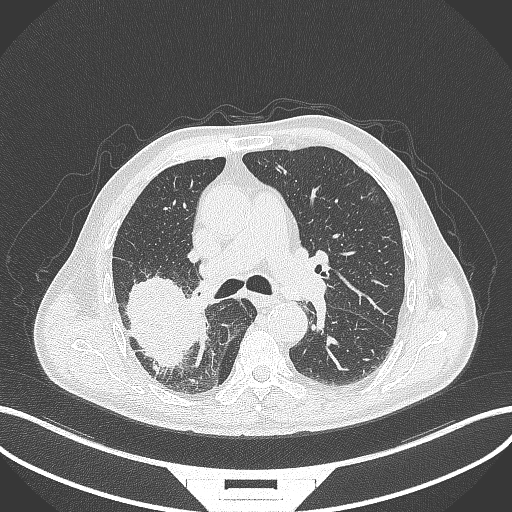
Chest CT, one axial slice. Slice 252 of 429 in the series (ordered by position). Reconstruction kernel B70f. 120 kVp. Lung window (W 1500 / L -600 HU). 512 × 512 image matrix, field of view 400 × 400 mm. Patient: male, 72 years. Case-level facts recorded for this patient, not image findings: clinical TNM (as recorded): T3 N2 M0.
Outlined on this slice (rectangle marked by the reading radiologist):
- lung tumour (recorded histology: adenocarcinoma): bounding box <120,271,202,376> (left, top, right, bottom; pixels)